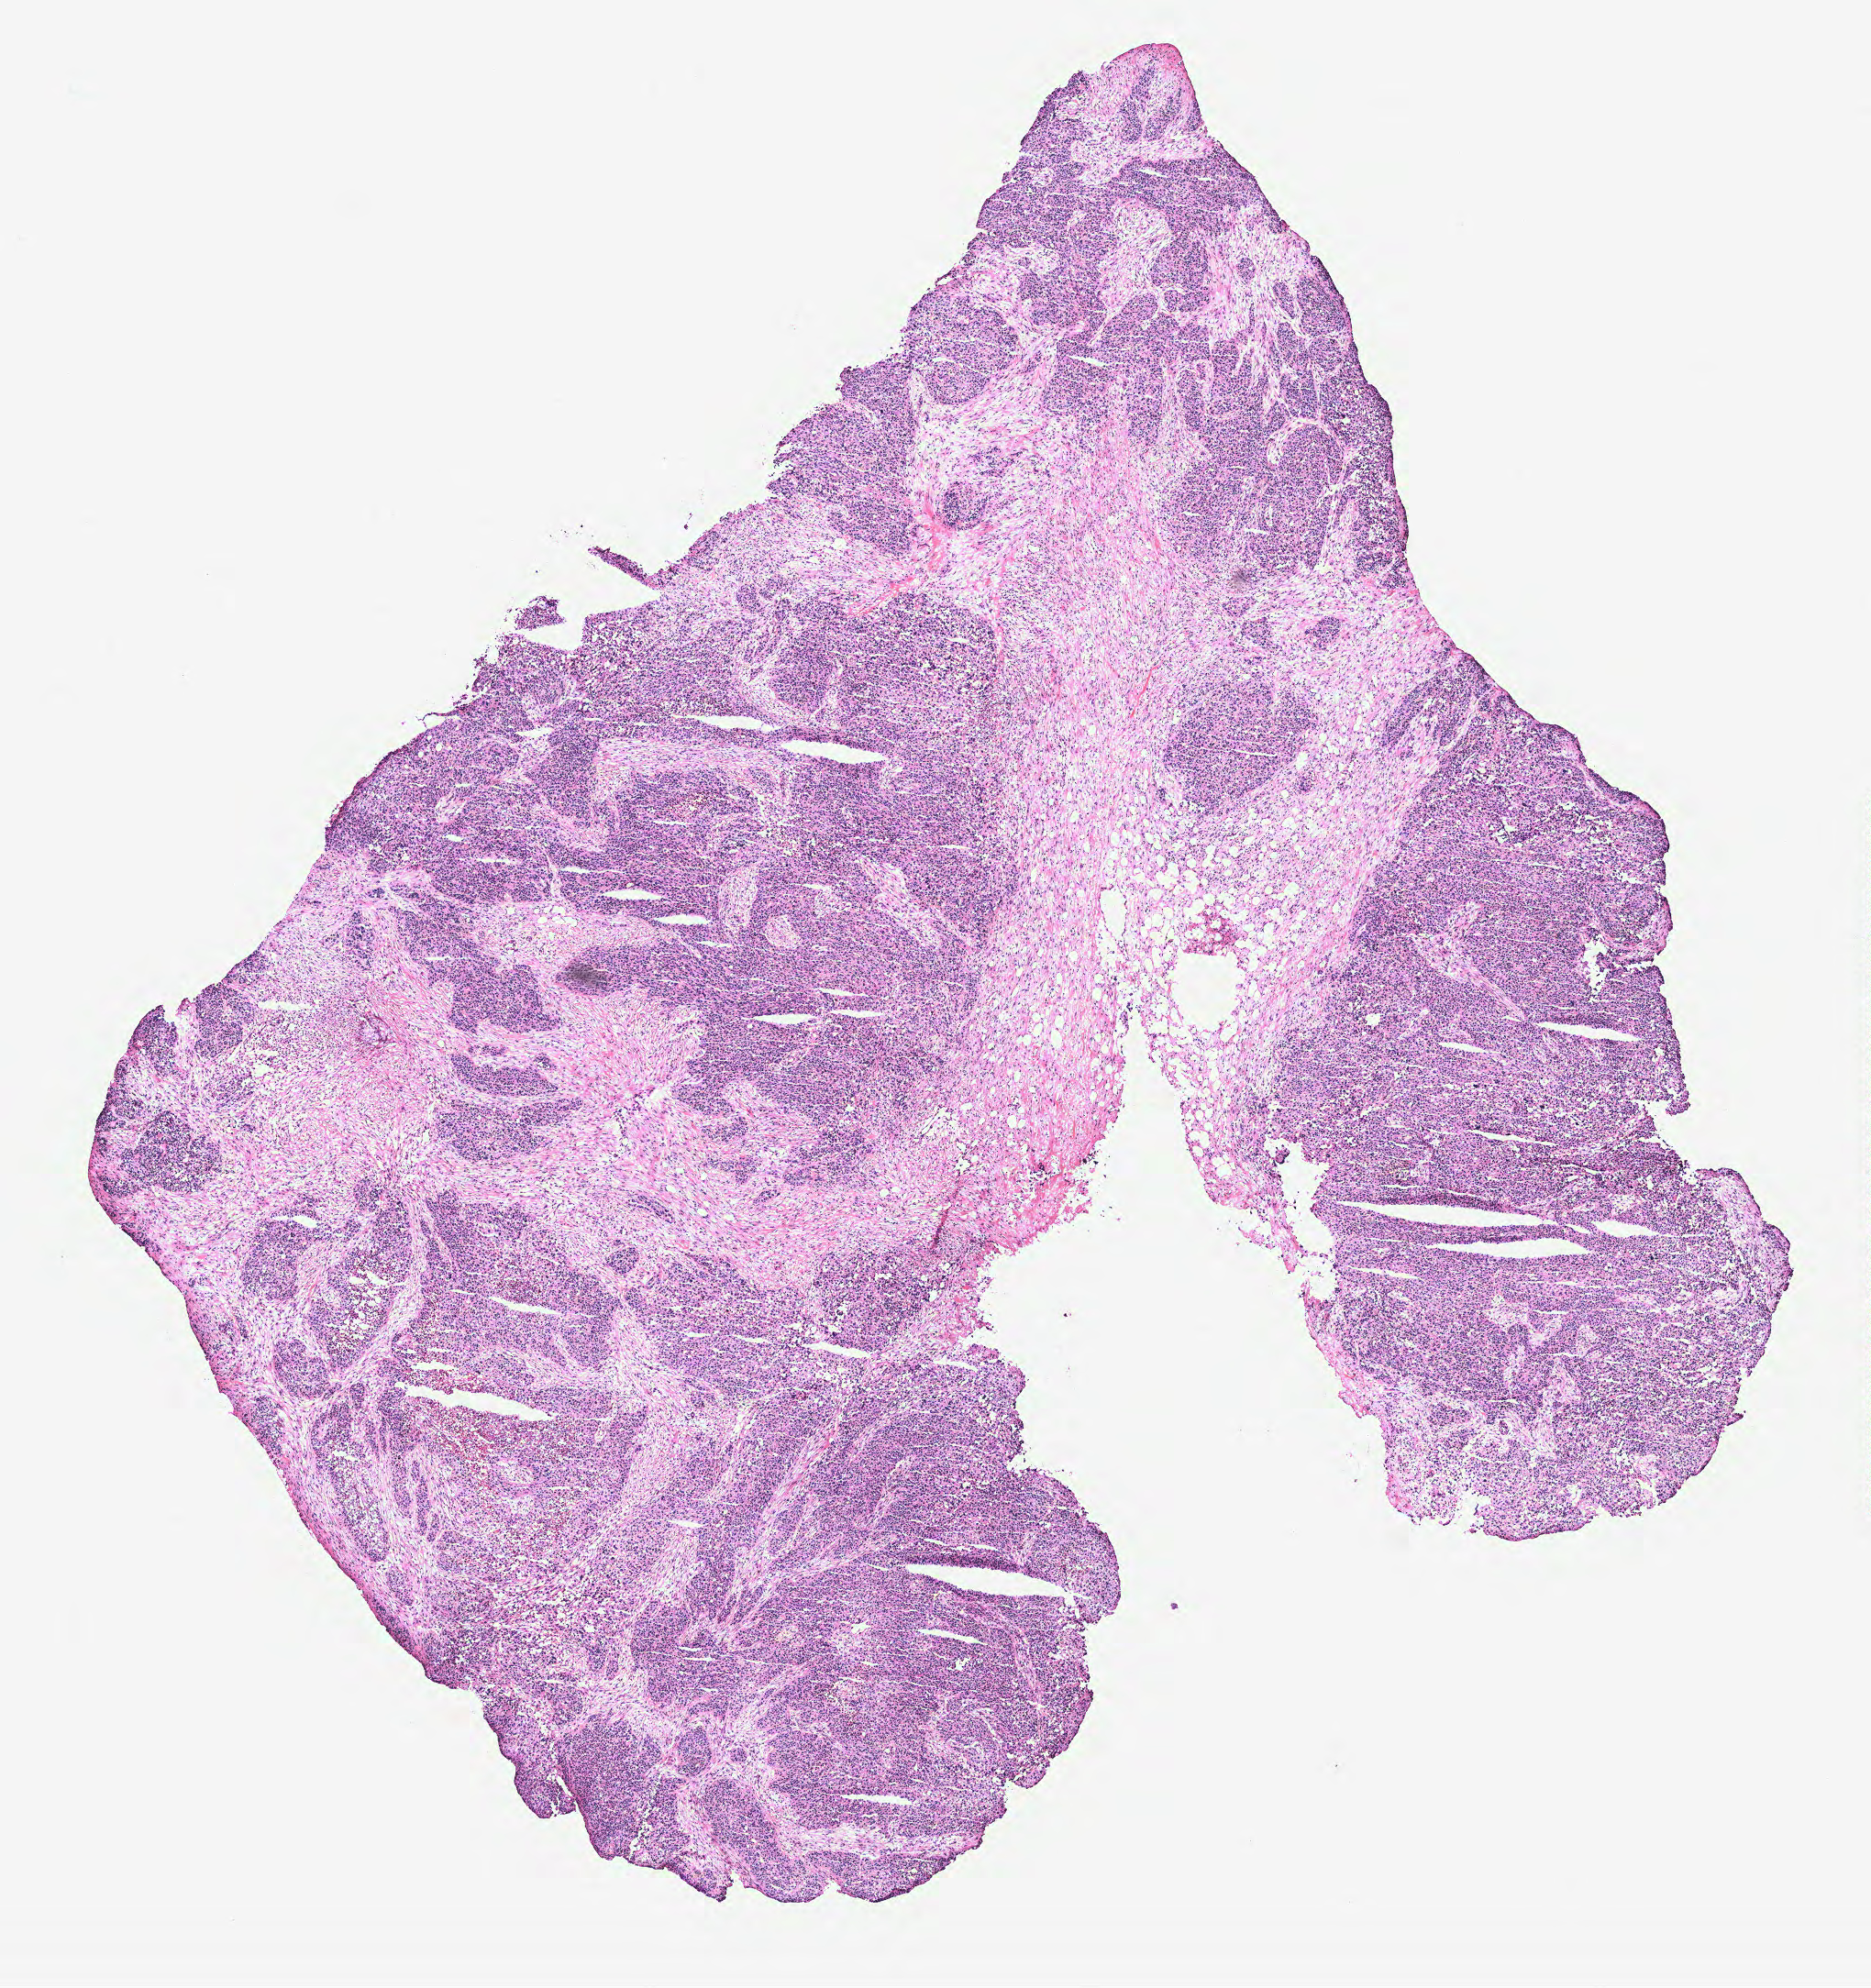
Digitized H&E-stained tissue section (whole slide), a low-resolution overview of the entire scanned area, about 8.2 x 8.7 mm (from a 40x scan), ovary, tissue type not recorded. Female patient.
Patient diagnosis: Serous adenocarcinoma, NOS.